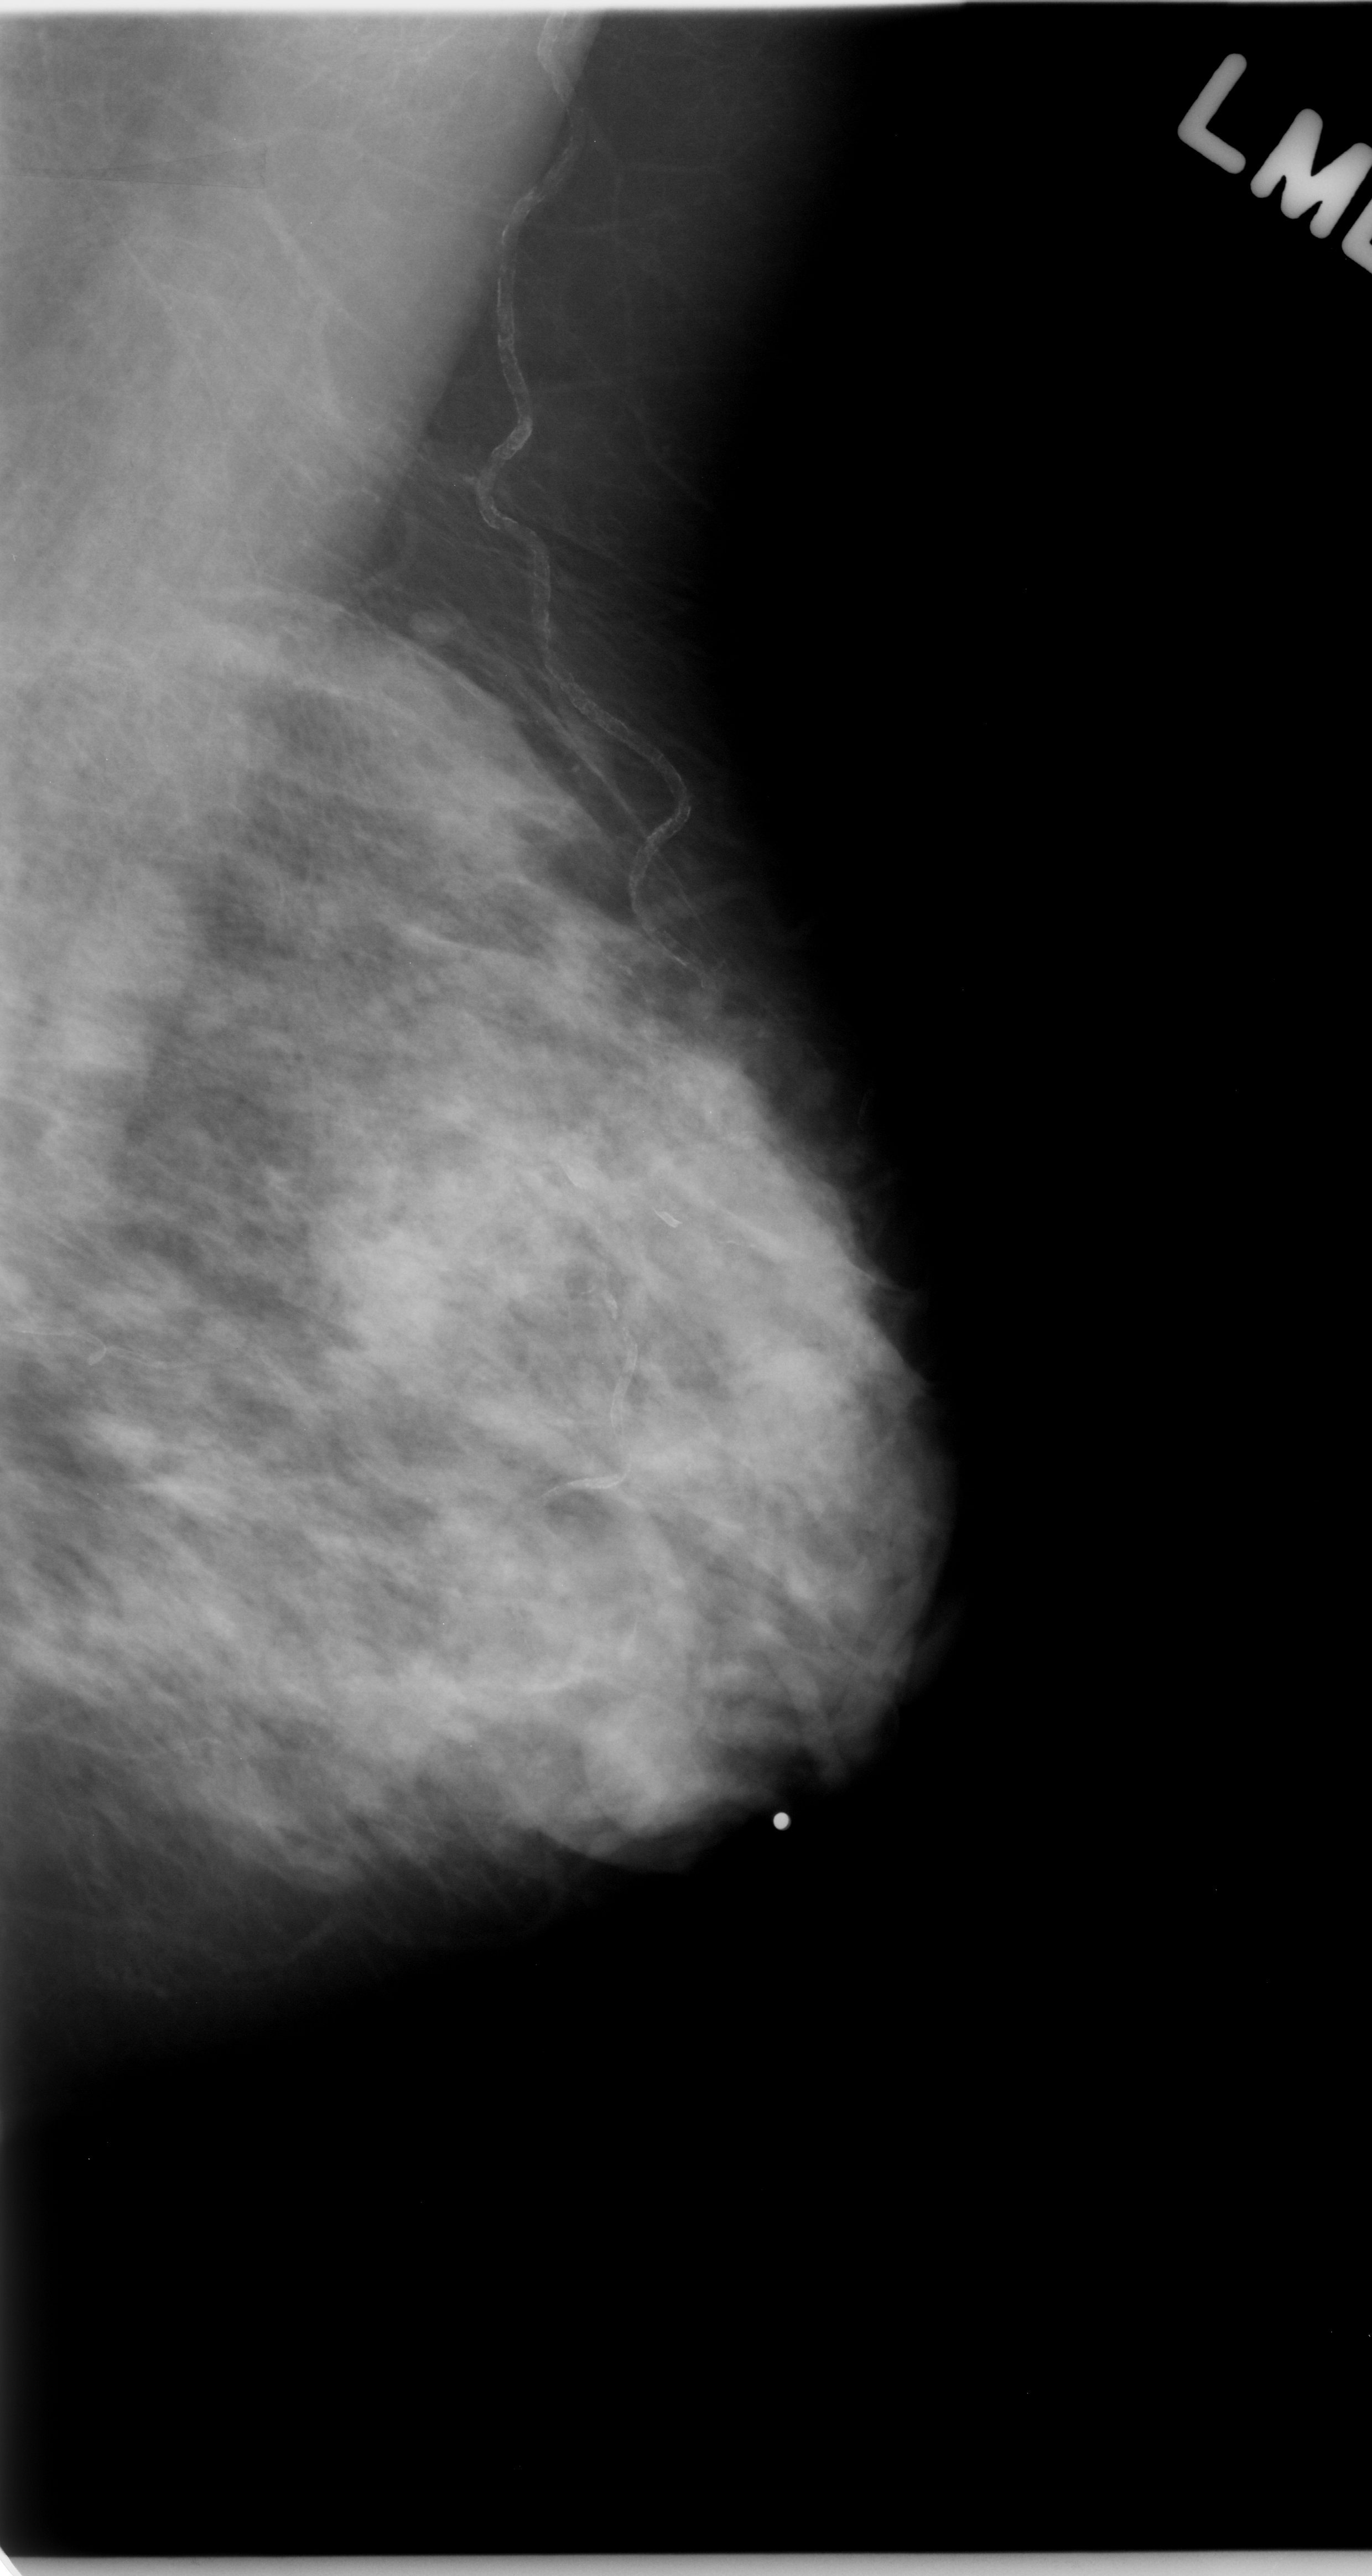
Mammogram (digitized film). Left breast. MLO view. BI-RADS breast density category 3 (scale 1–4). 1372 × 2576 image matrix.
Marked abnormalities (boxes around the expert regions of interest):
- mass, shape oval, margins circumscribed; BI-RADS assessment category 3; subtlety rating 5 on a 1 (subtle) to 5 (obvious) scale; pathology (as recorded): benign: bounding box [x1, y1, x2, y2] px = [568, 1705, 751, 1841]